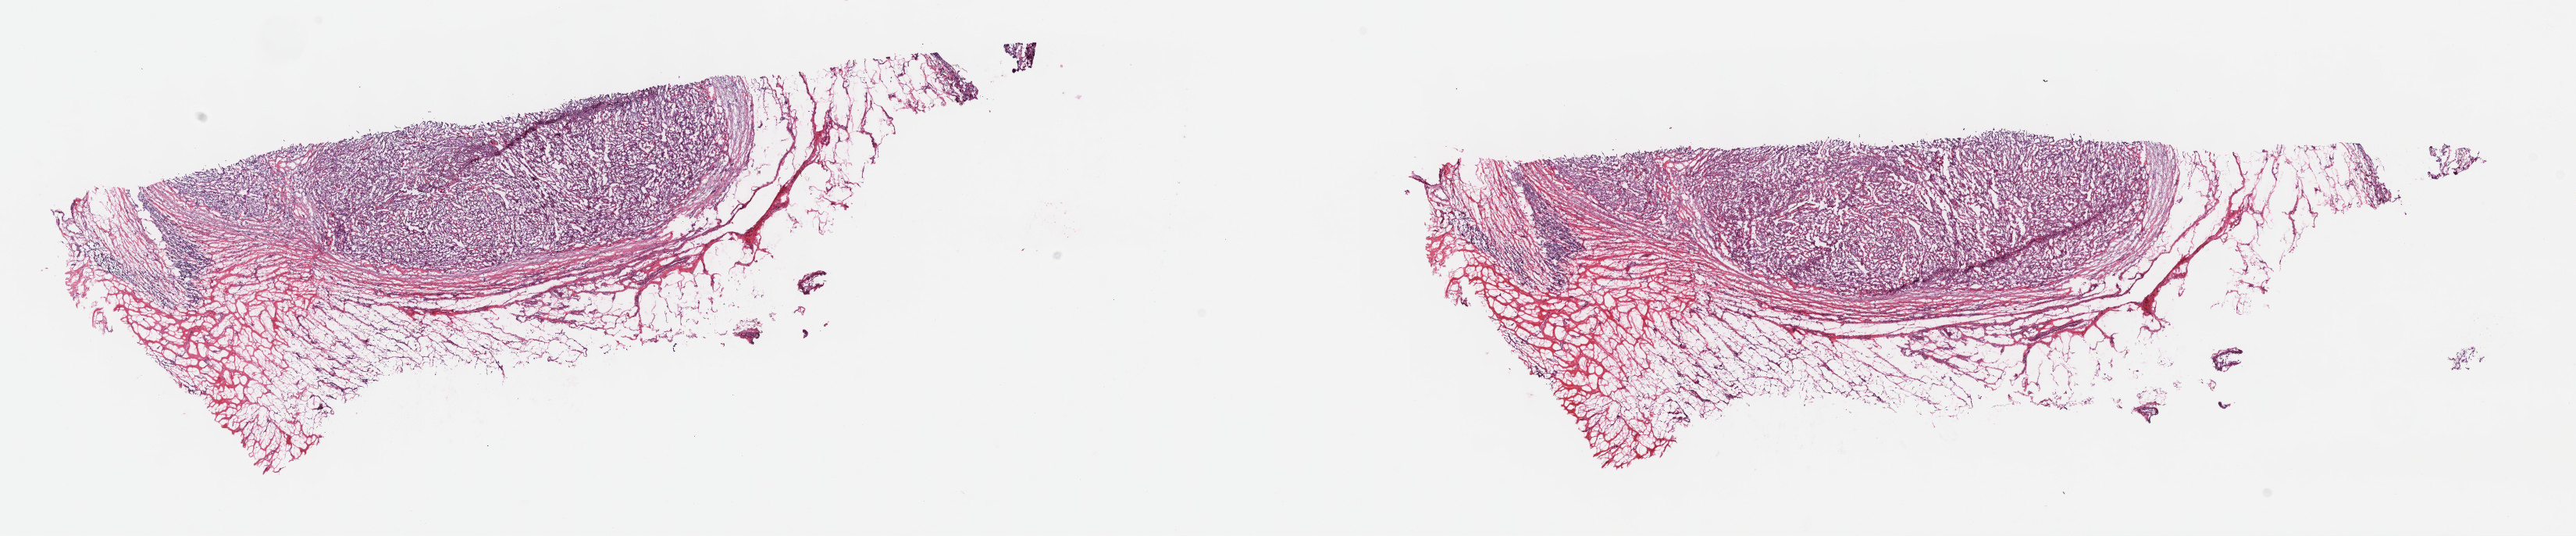
Whole-slide histology image, H&E — a low-resolution overview of the entire scanned area, about 26.7 x 5.5 mm (acquisition: 40x scan); frozen section; mesothelium, primary tumour sample. Male patient; age at initial diagnosis 67 years. Pathologist review of this section (percent, as recorded): tumour cells 60%, tumour nuclei 70%, normal cells 30%, stromal cells 10%, necrosis 0%. Inflammatory infiltration, as recorded: lymphocyte infiltration 0%, monocyte infiltration 0%, neutrophil infiltration 0%.
AJCC pathologic stage: III. Diagnosis: Epithelioid mesothelioma, malignant (pleura, NOS).